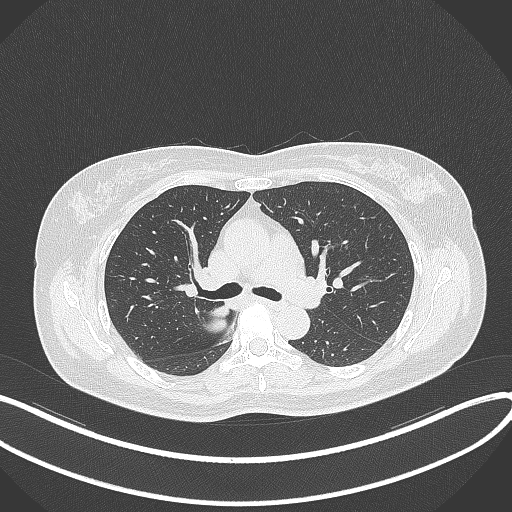
Chest CT, one axial slice; position 232 of 331 along the scan axis; reconstruction kernel B70f; 120 kVp; lung window (W 1500 / L -600 HU); 1 mm slice thickness; 512 × 512 image matrix, field of view 400 × 400 mm. Patient: female, 54 years. From the clinical record (not read from this slice): clinical TNM (as recorded): T4 N0 M0.
Outlined on this slice (rectangle marked by the reading radiologist):
- lung tumour (recorded histology: adenocarcinoma): bounding box [x1, y1, x2, y2] px = [200, 305, 232, 336]